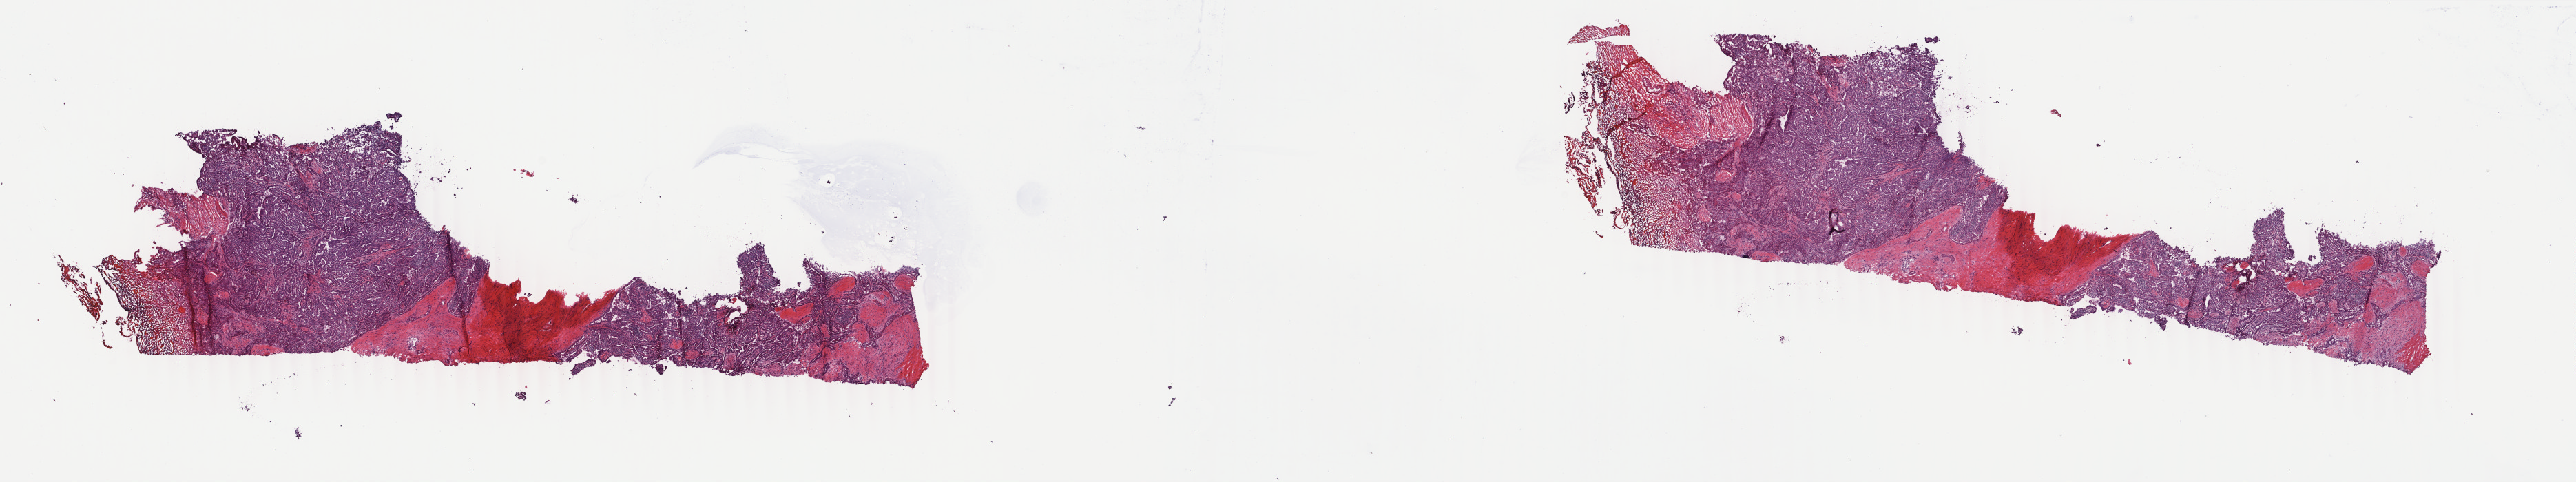
Whole-slide histology image, H&E-stained, low-resolution overview of the scanned area, about 29.7 x 5.6 mm (slide scanned at 40x). Frozen section. Thyroid, primary tumour sample. Female, age 51 years at initial diagnosis. Slide review estimates, as recorded: tumour cells 75%, tumour nuclei 75%.
Diagnosis: Papillary carcinoma, columnar cell (thyroid gland).